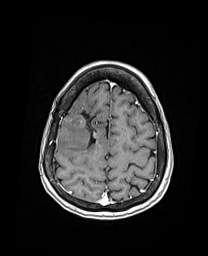
Brain MRI from a brain-tumour surgery series, one axial slice; T1-weighted post-contrast; 1 mm slice thickness; 208 × 256 image matrix, field of view 208 × 256 mm. Case-level facts recorded for this patient, not image findings: histopathology: Oligodendroglioma; WHO grade: 3; IDH mutation: yes; tumour location: Right Frontal.
Structures marked on this image (expert manual segmentation):
- previous resection cavity: box from (x=80, y=109) to (x=96, y=148) px